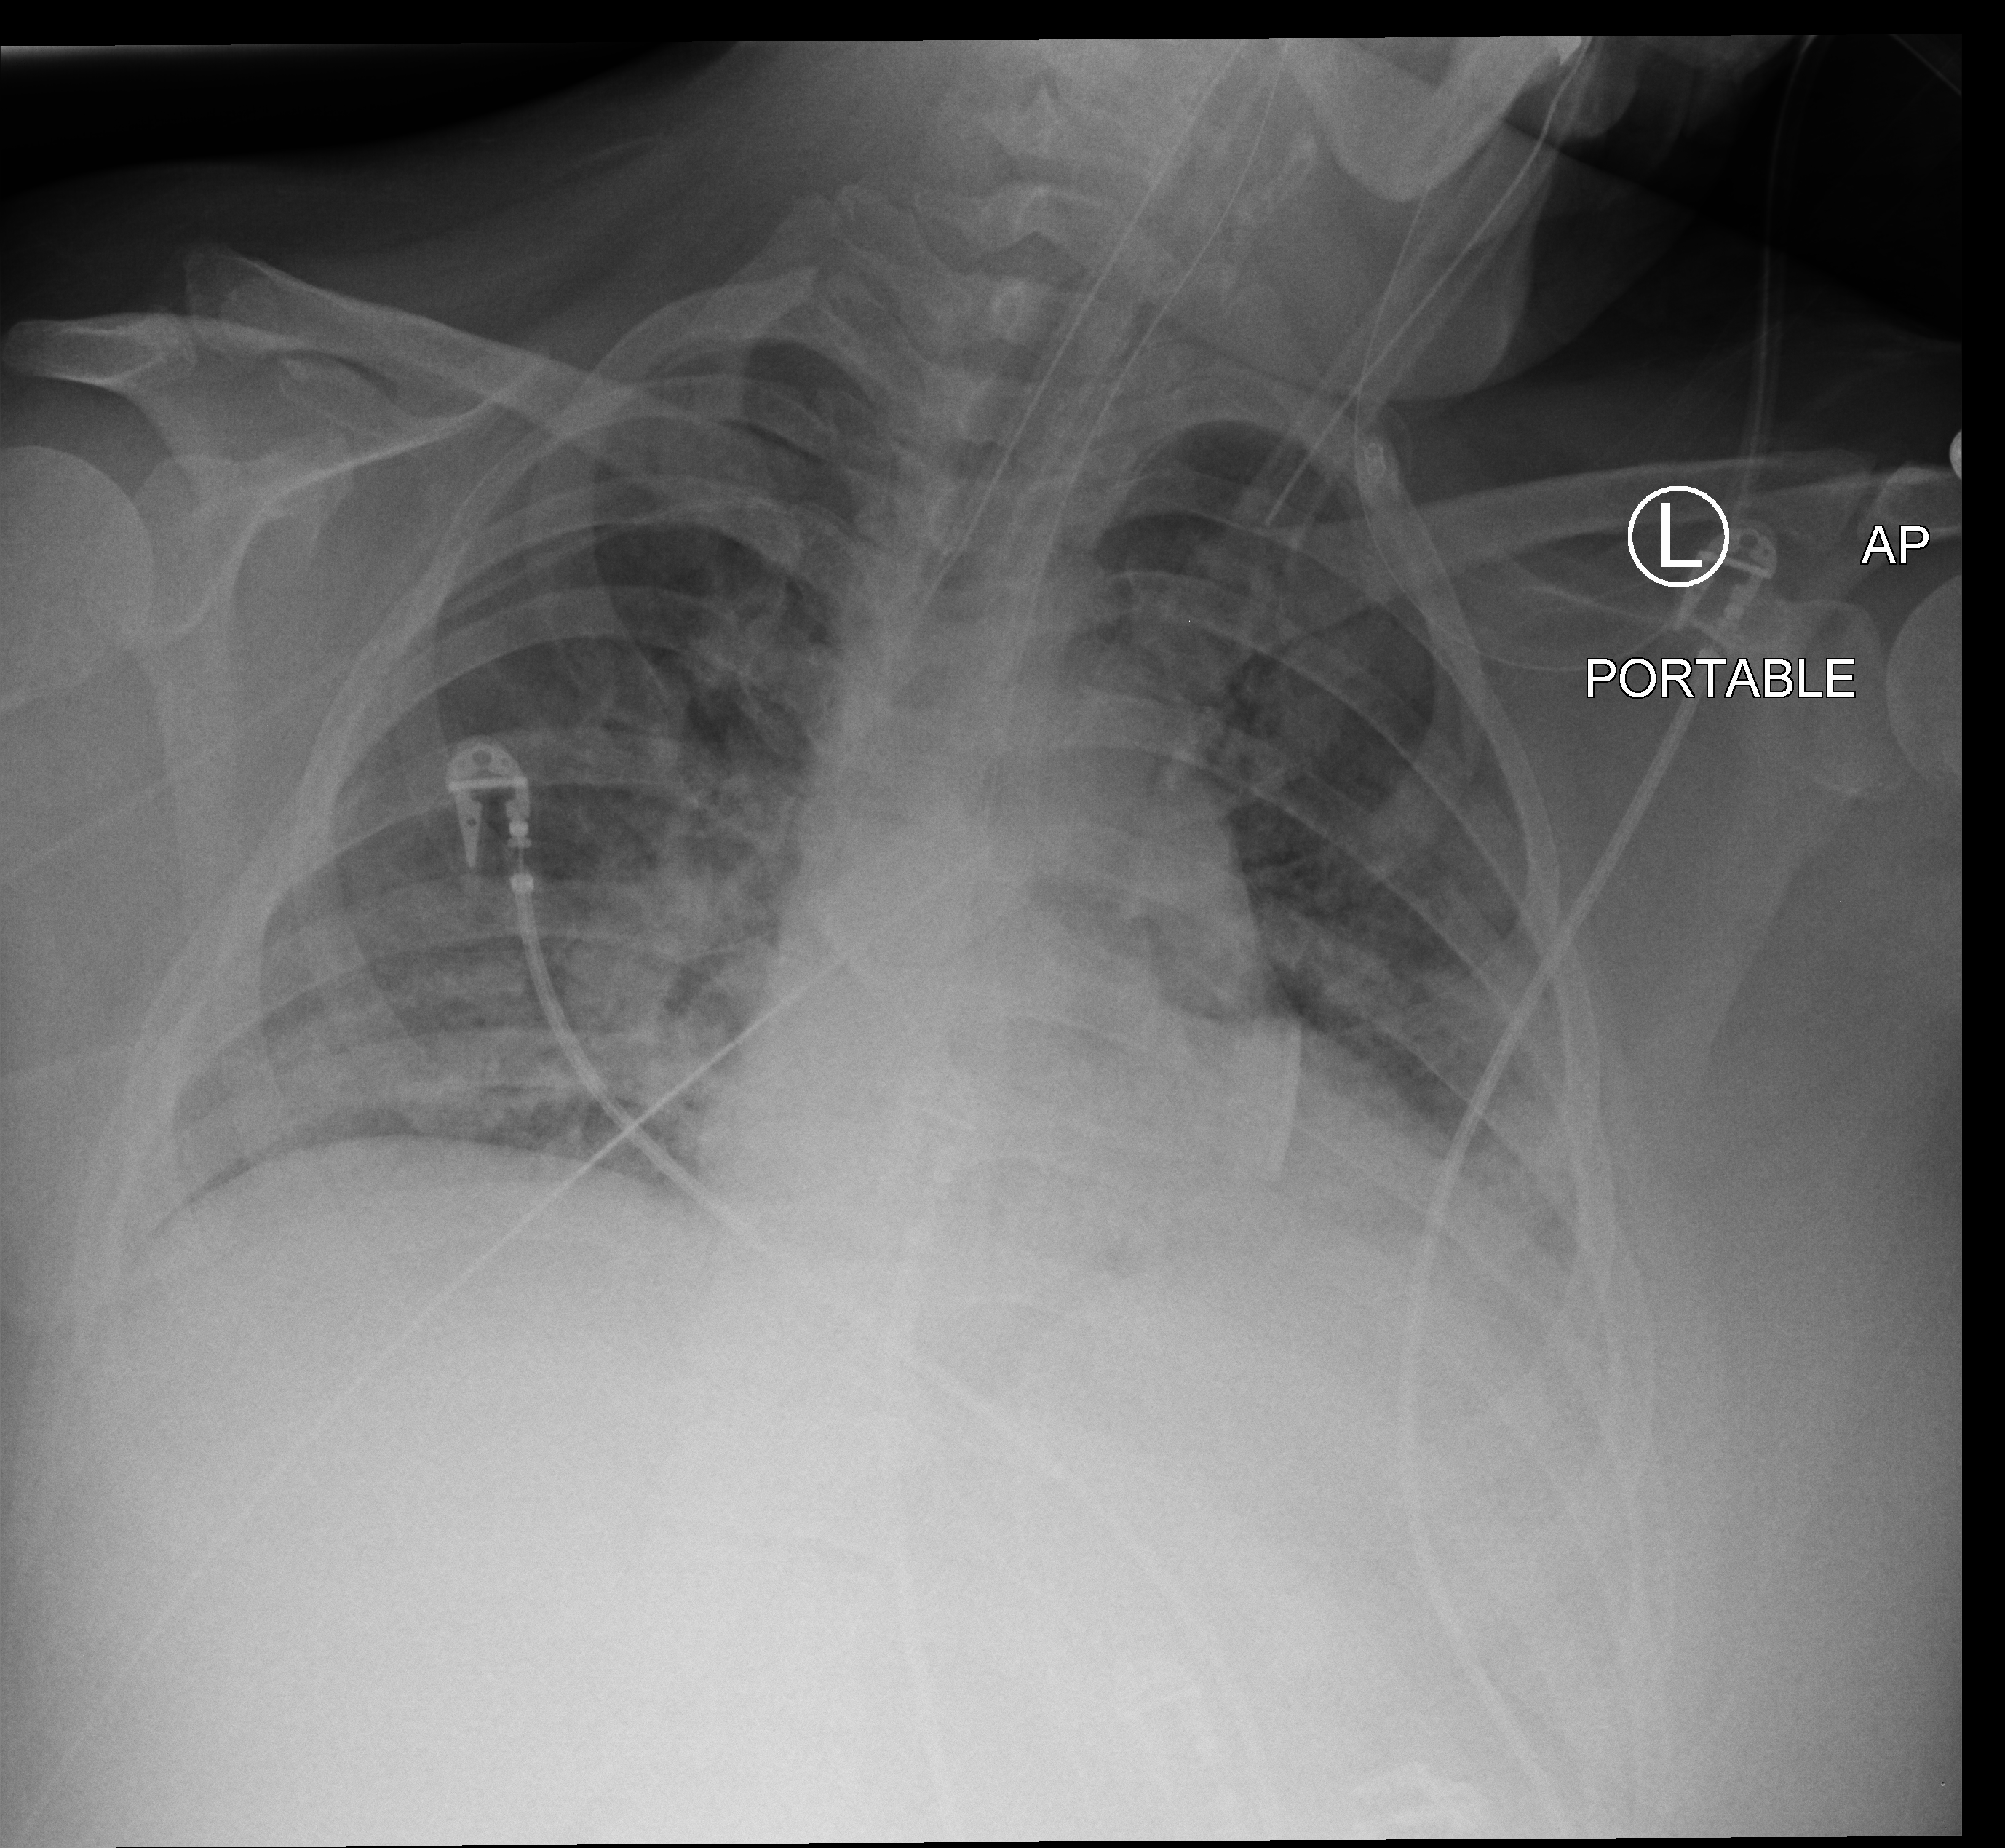
Portable chest radiograph; anteroposterior (AP) projection. Patient hospitalised with COVID-19; female, aged 18–59 years.
Admission-level facts for this patient (not findings on this image; timing relative to this image not recorded): other chronic lung disease (admission record): no; admitted to intensive care during this hospital stay: yes; chronic kidney disease (admission record): no.